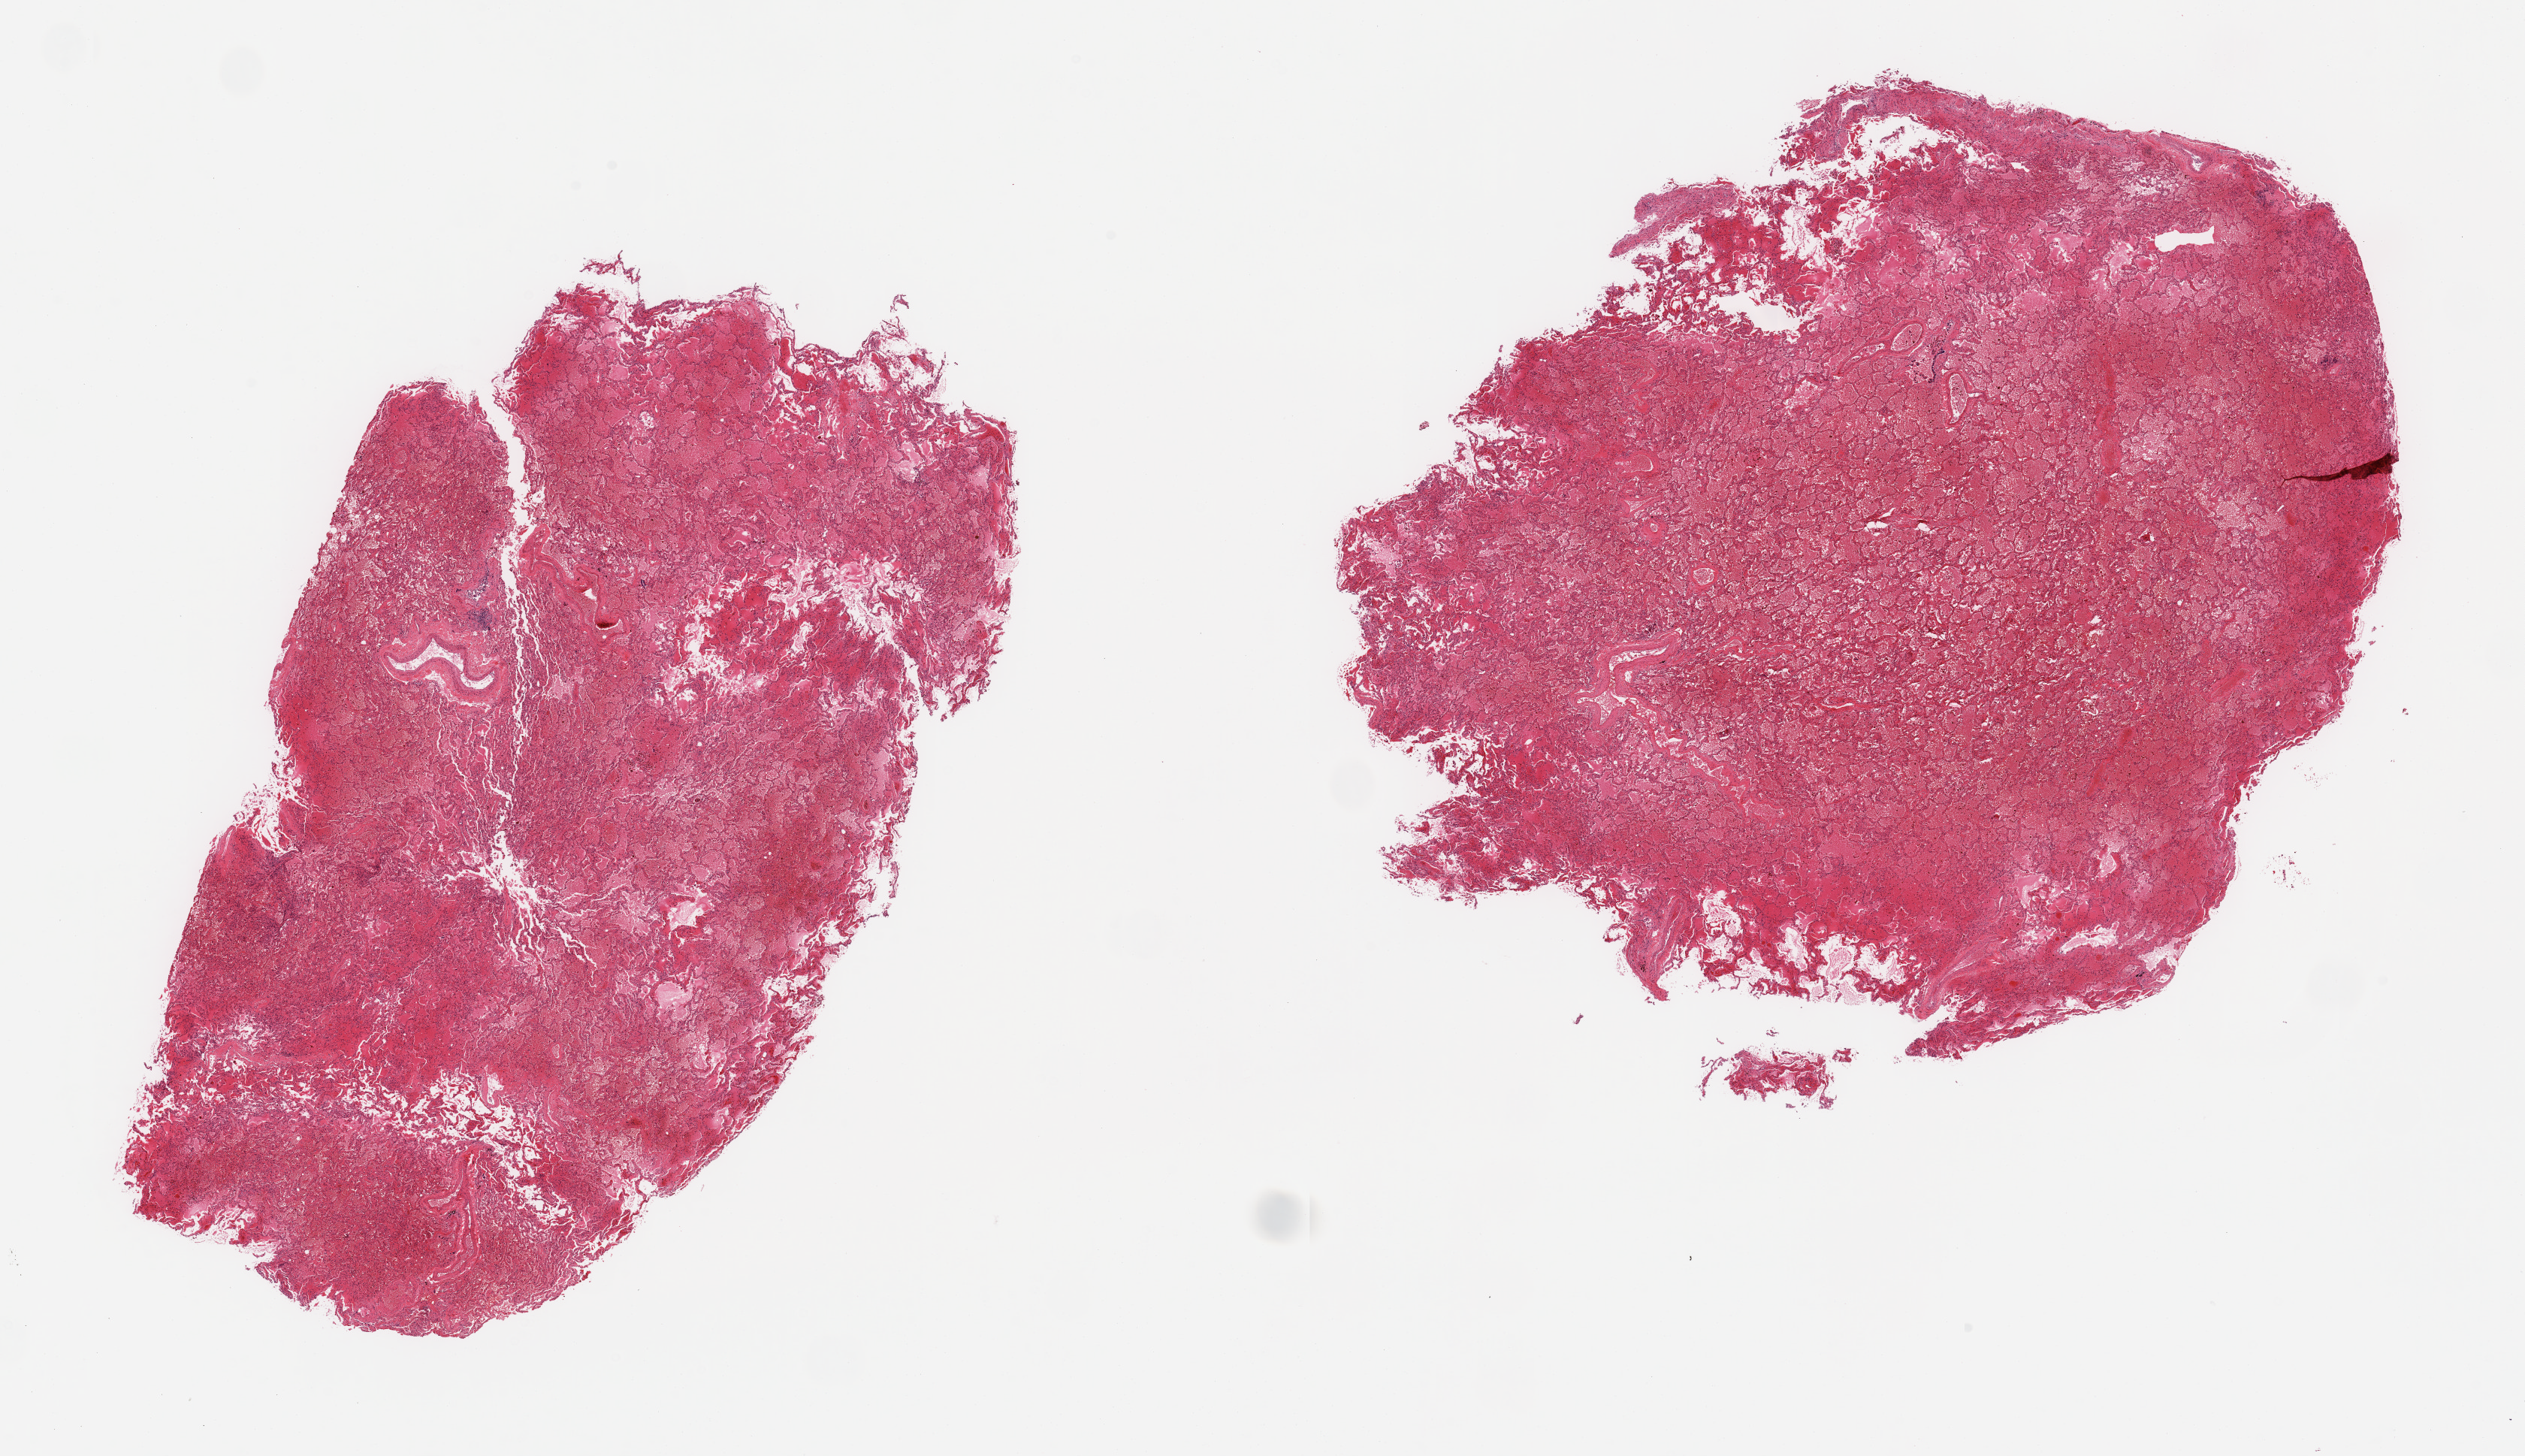
Digitized hematoxylin and eosin (H&E)-stained section — a low-resolution overview of the entire scanned area, about 26.6 x 15.3 mm (slide scanned at 20x), PAXgene-fixed paraffin-embedded (PFPE) section, sampled site (target tissue): lung, tissue donor sample. Male donor.
Pathologist's review note for this sample: 2 pieces, severe congestion.